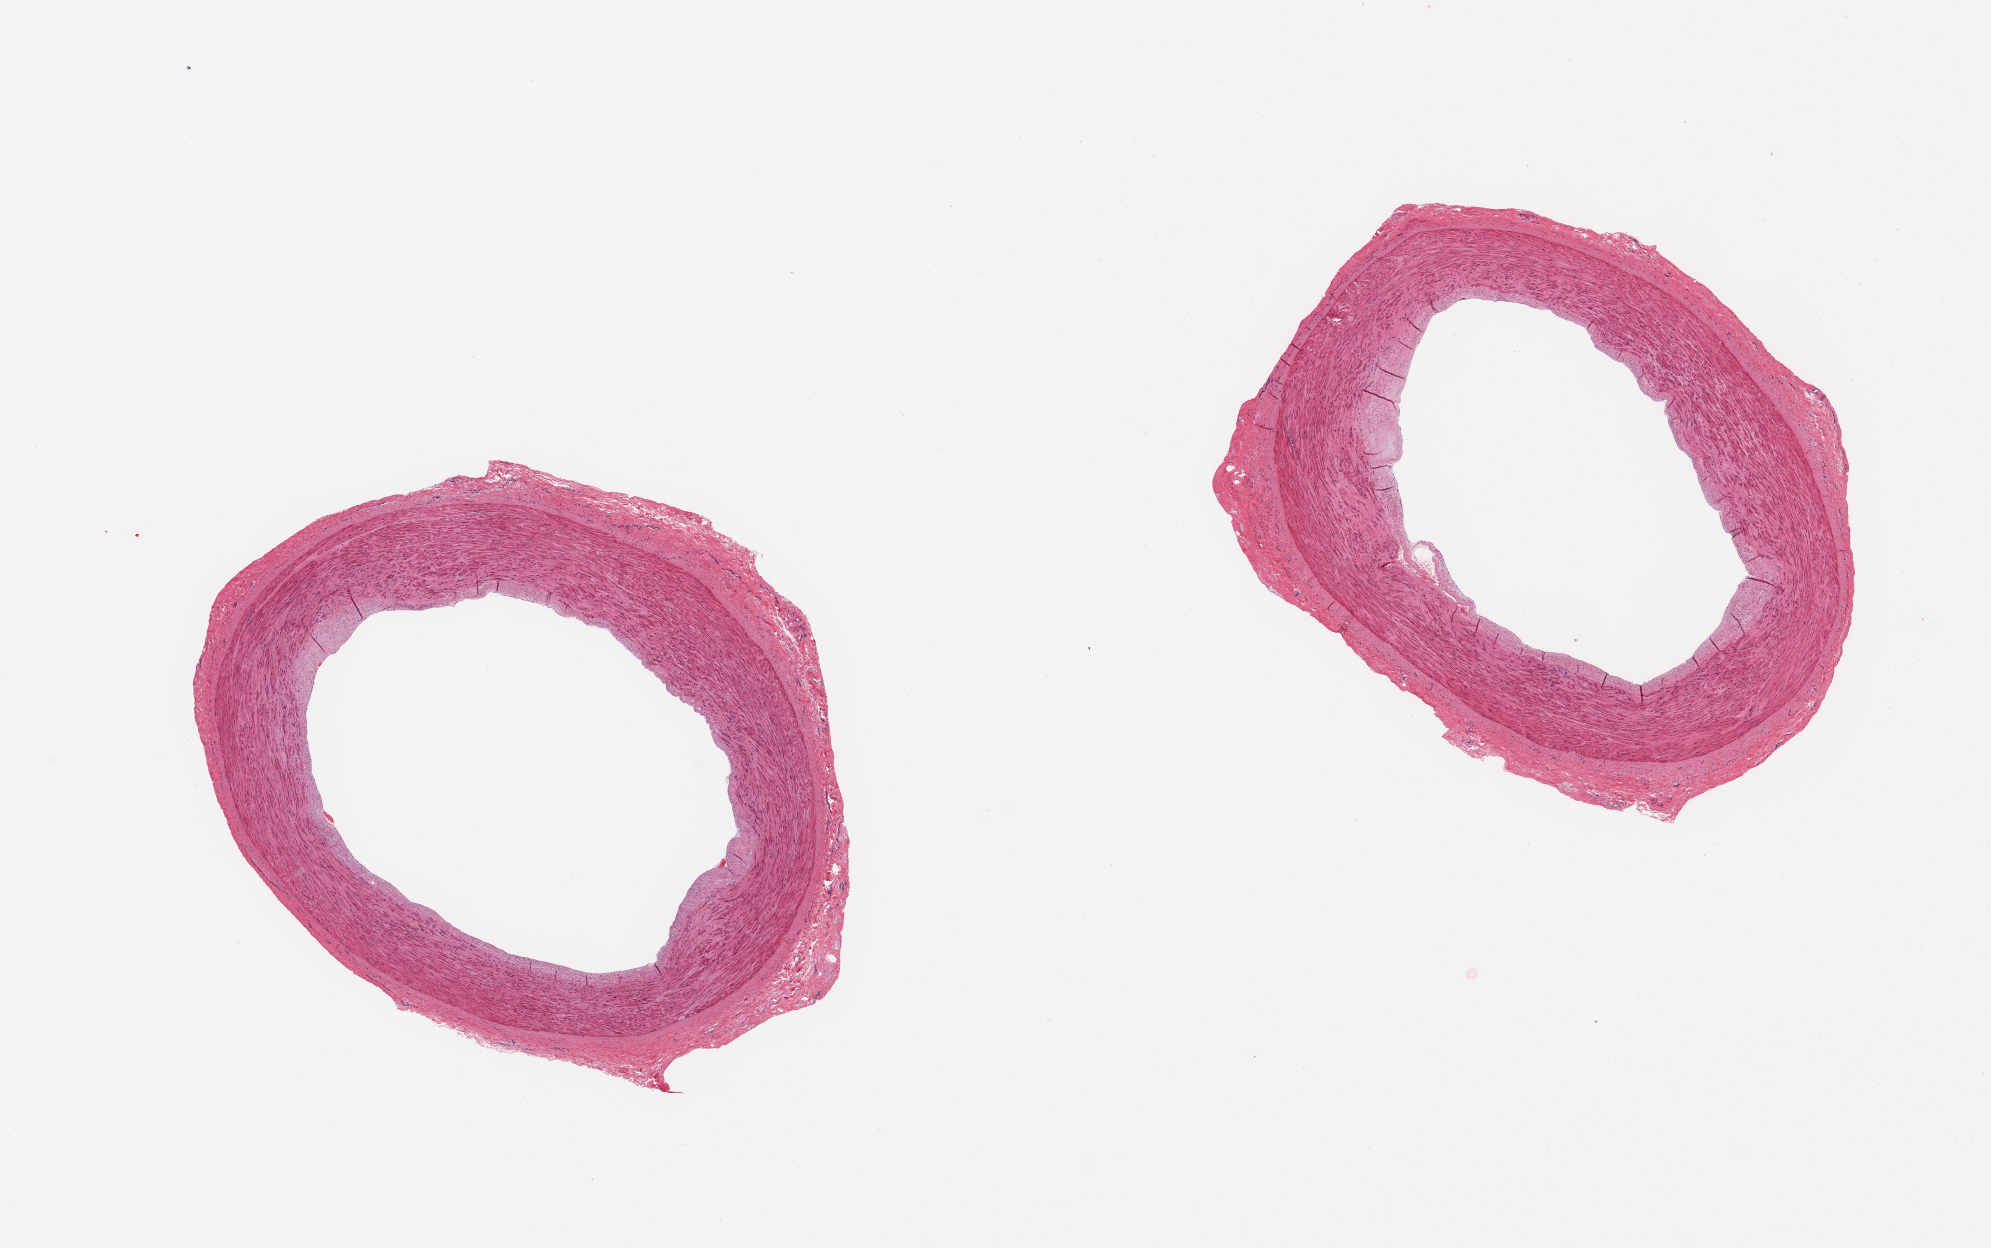
H&E whole-slide image — low-resolution overview of the scanned area, about 15.8 x 9.9 mm. PAXgene-fixed, paraffin-embedded tissue. Section of tibial artery (target tissue). Donor tissue sample.
* review note (as recorded): 2 pieces, no adherent fat; trace atherosis